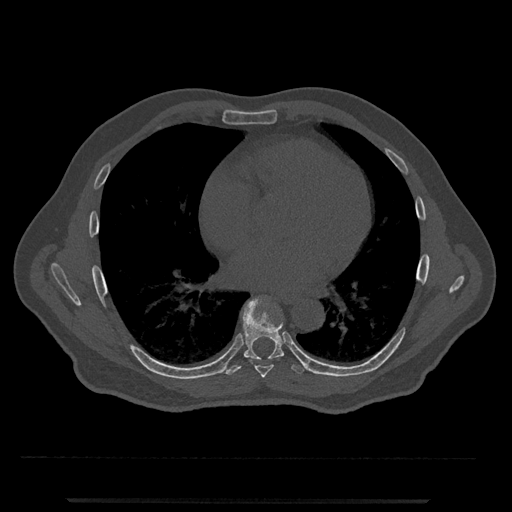
CT including the spine, one axial slice. Position 653 of 797 along the scan axis. 120 kVp. Bone window (W 1800 / L 400 HU). 0.5 mm slice thickness. 512 × 512 image matrix, field of view 419 × 419 mm. Patient: male, 63 years. From the clinical record (not read from this slice): primary cancer: prostate.
Outlined on this slice (semi-automatically segmented with operator editing):
- T7 vertebra: box from (x=255, y=365) to (x=273, y=379) px
- T8 vertebra: (x=225, y=296)–(x=305, y=375)